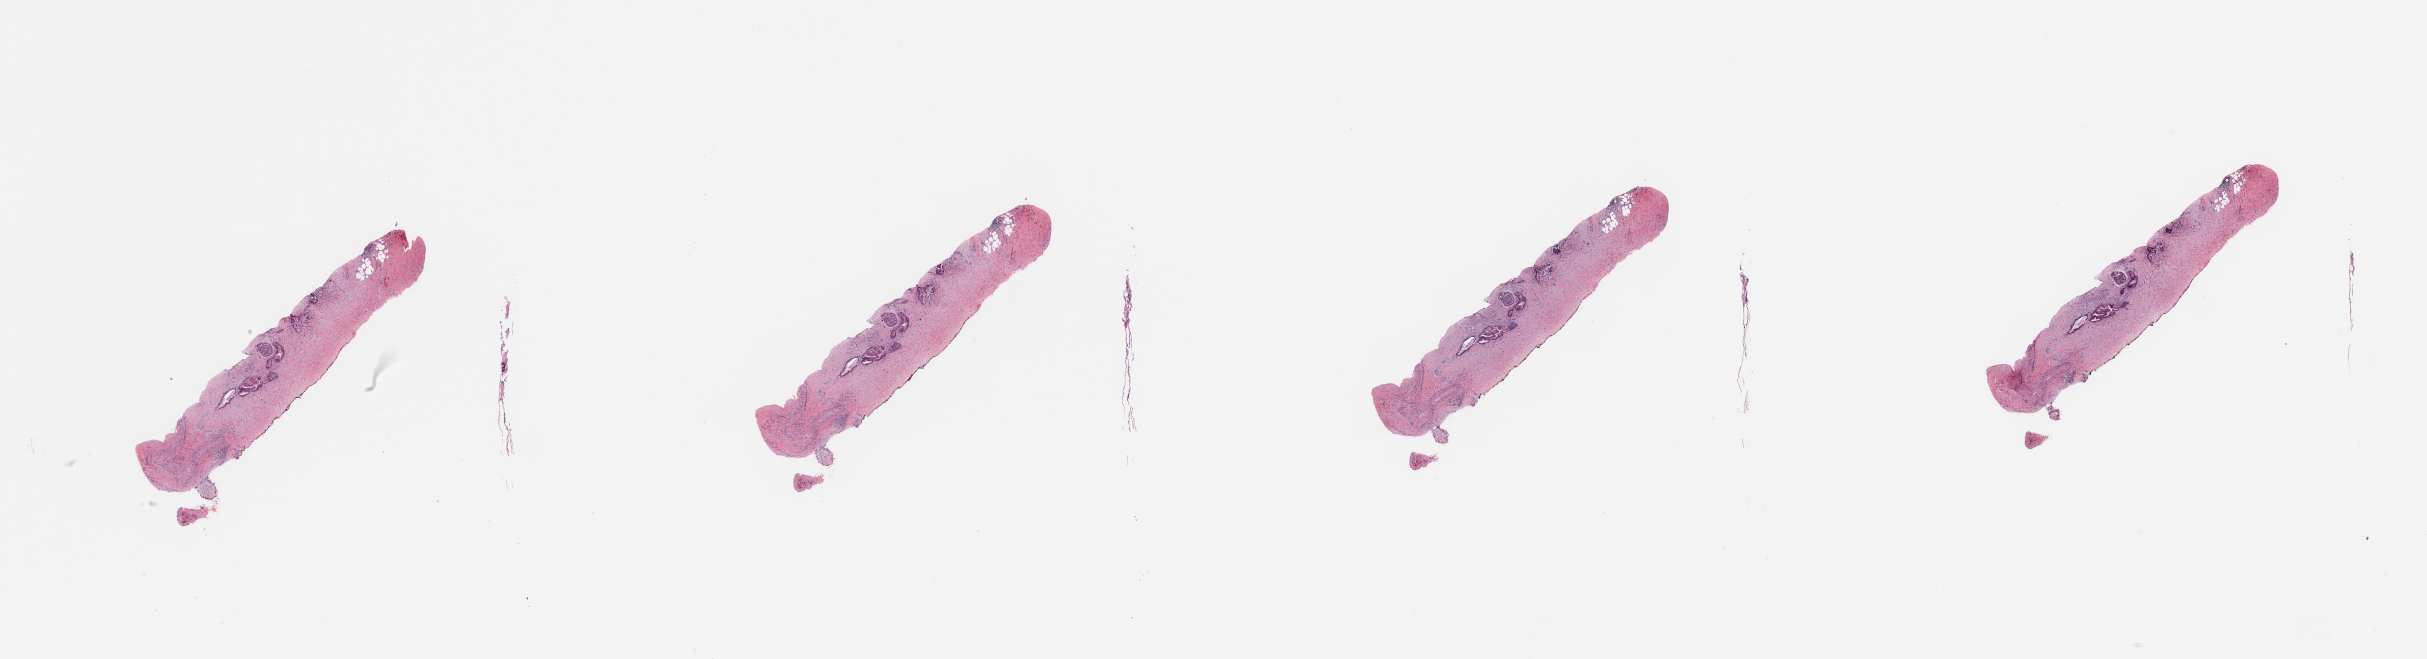
Digitized H&E tissue section (whole slide), whole scanned area (about 38.4 x 10.4 mm) shown as a low-resolution overview, tumour tissue sample, sampled site: pancreas. Patient: male, age 62 years. Histologic grade: G3 (poorly differentiated). Pathologist review of this section (percent, as recorded): tumour nuclei 5%, necrosis 0%.
AJCC pathologic stage: IIA. Diagnosis: Infiltrating duct carcinoma, NOS.